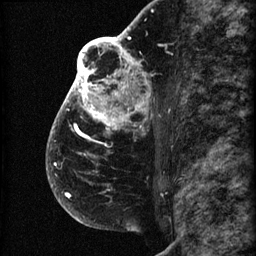
Breast MRI (dynamic contrast-enhanced), one sagittal slice. 3 images stored at this slice position (order not interpretable as contrast timing). 1.5 T. TE 4.2 ms, TR 22.7 ms. 2 mm slice thickness. 256 × 256 image matrix. Female patient, age 48 years. Case-level facts recorded for this patient, not image findings: setting: breast cancer imaged before/during neoadjuvant chemotherapy; receptor status: triple-negative.
Annotated regions visible in this slice (semi-automatically segmented with operator editing):
- analysis volume of interest (the breast-tissue region the enhancement analysis was run in; not a lesion): bounding box [x1, y1, x2, y2] px = [46, 30, 173, 207]
- tumour enhancement mask (voxels above the 90 % enhancement threshold inside the analysis volume of interest): [47, 30, 151, 198]